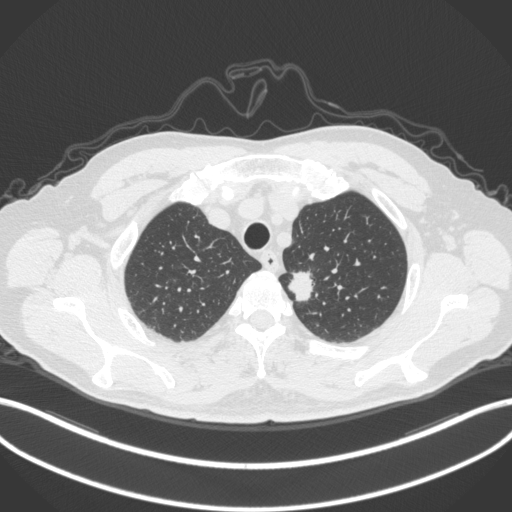
Chest CT, one axial slice; position 316 of 382 along the scan axis; reconstruction kernel B31f; lung window (W 1500 / L -600 HU); 1 mm slice thickness; 512 × 512 image matrix, field of view 400 × 400 mm. Male patient, age 64 years. Case-level facts recorded for this patient, not image findings: clinical TNM (as recorded): T1c N0 M0.
Outlined on this slice (rectangle marked by the reading radiologist):
- lung tumour (recorded histology: adenocarcinoma): bounding box (x1, y1, x2, y2) in pixels: (285, 265, 323, 309)